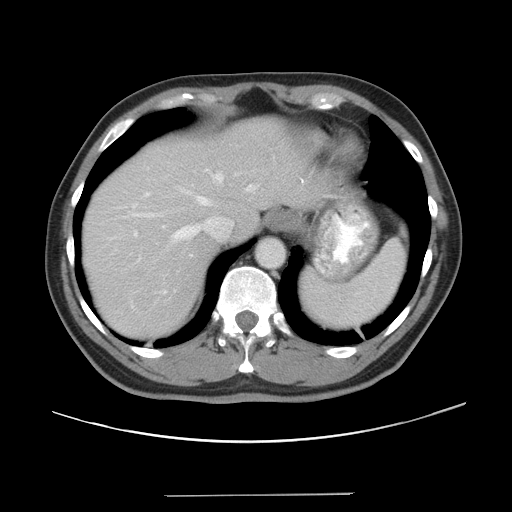
Contrast-enhanced abdominal CT, one axial slice; reconstruction kernel STANDARD; 120 kVp; intravenous contrast given; soft-tissue window (W 400 / L 40 HU); 5 mm slice thickness; 512 × 512 image matrix, field of view 409 × 409 mm. Male patient, age 65 years. From the clinical record (not read from this slice): diagnosis: colorectal cancer liver metastases, imaged before liver resection; multiple liver metastases: no; largest metastasis: 3.8 cm; chemotherapy before resection: yes.
Annotated regions visible in this slice (outlined manually by an expert reader):
- hepatic veins: box from (x=139, y=172) to (x=255, y=242) px
- liver: (x=83, y=120)–(x=314, y=339)
- planned liver remnant (the part of the liver to remain after resection): (x=83, y=120)–(x=313, y=322)
- portal vein (with intrahepatic branches): (x=134, y=192)–(x=150, y=236)